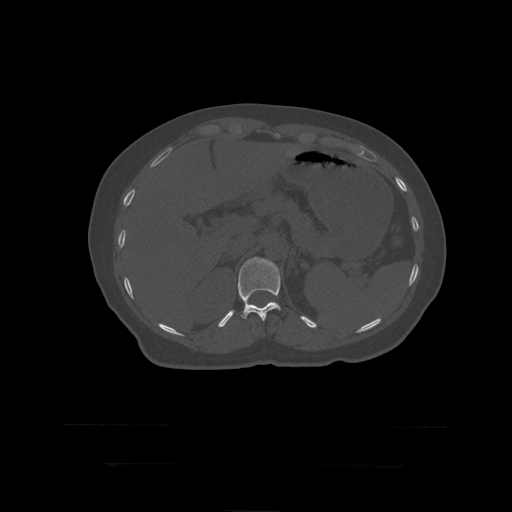
CT including the spine, one axial slice; position 197 of 399 along the scan axis; reconstruction kernel STANDARD; bone window (W 1800 / L 400 HU); 512 × 512 image matrix, field of view 450 × 450 mm. Patient age 41 years. Case-level facts recorded for this patient, not image findings: primary cancer: breast.
Outlined on this slice (semi-automatic segmentation, software-assisted and operator-edited):
- T12 vertebra: box from (x=238, y=257) to (x=281, y=321) px